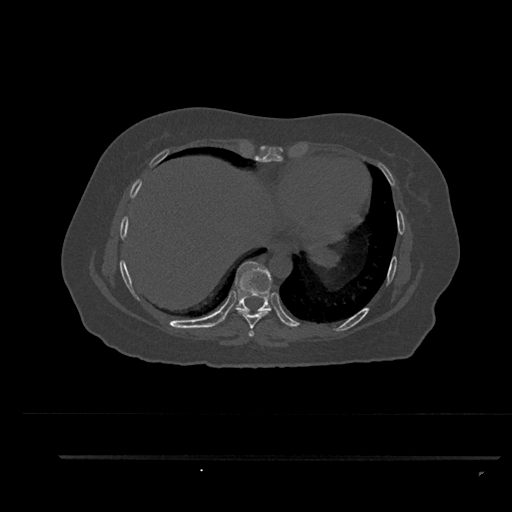
CT including the spine, one axial slice; position 439 of 797 along the scan axis; reconstruction kernel Br40s/3; bone window (W 1800 / L 400 HU); 0.5 mm slice thickness; 512 × 512 image matrix, field of view 408 × 408 mm. Female patient, age 44 years. From the clinical record (not read from this slice): primary cancer: renal; vertebrae with lytic lesions (as recorded): L1.
Structures marked on this image (semi-automatically segmented with operator editing):
- T7 vertebra: bounding box [x1, y1, x2, y2] px = [248, 330, 255, 337]
- T8 vertebra: [237, 310, 270, 329]
- T9 vertebra: [234, 261, 272, 311]